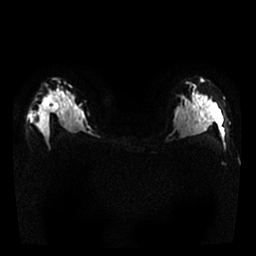
Breast MRI, one axial slice. Diffusion-weighted series; image 2 of 4 stored at this slice position (different b-values; order by instance number). 1.5 T. 4 mm slice thickness. 256 × 256 image matrix, field of view 320 × 320 mm. Female patient.
Annotated regions visible in this slice (expert manual segmentation):
- tumour on diffusion-weighted imaging: bounding box (x1, y1, x2, y2) in pixels: (42, 96, 57, 111)